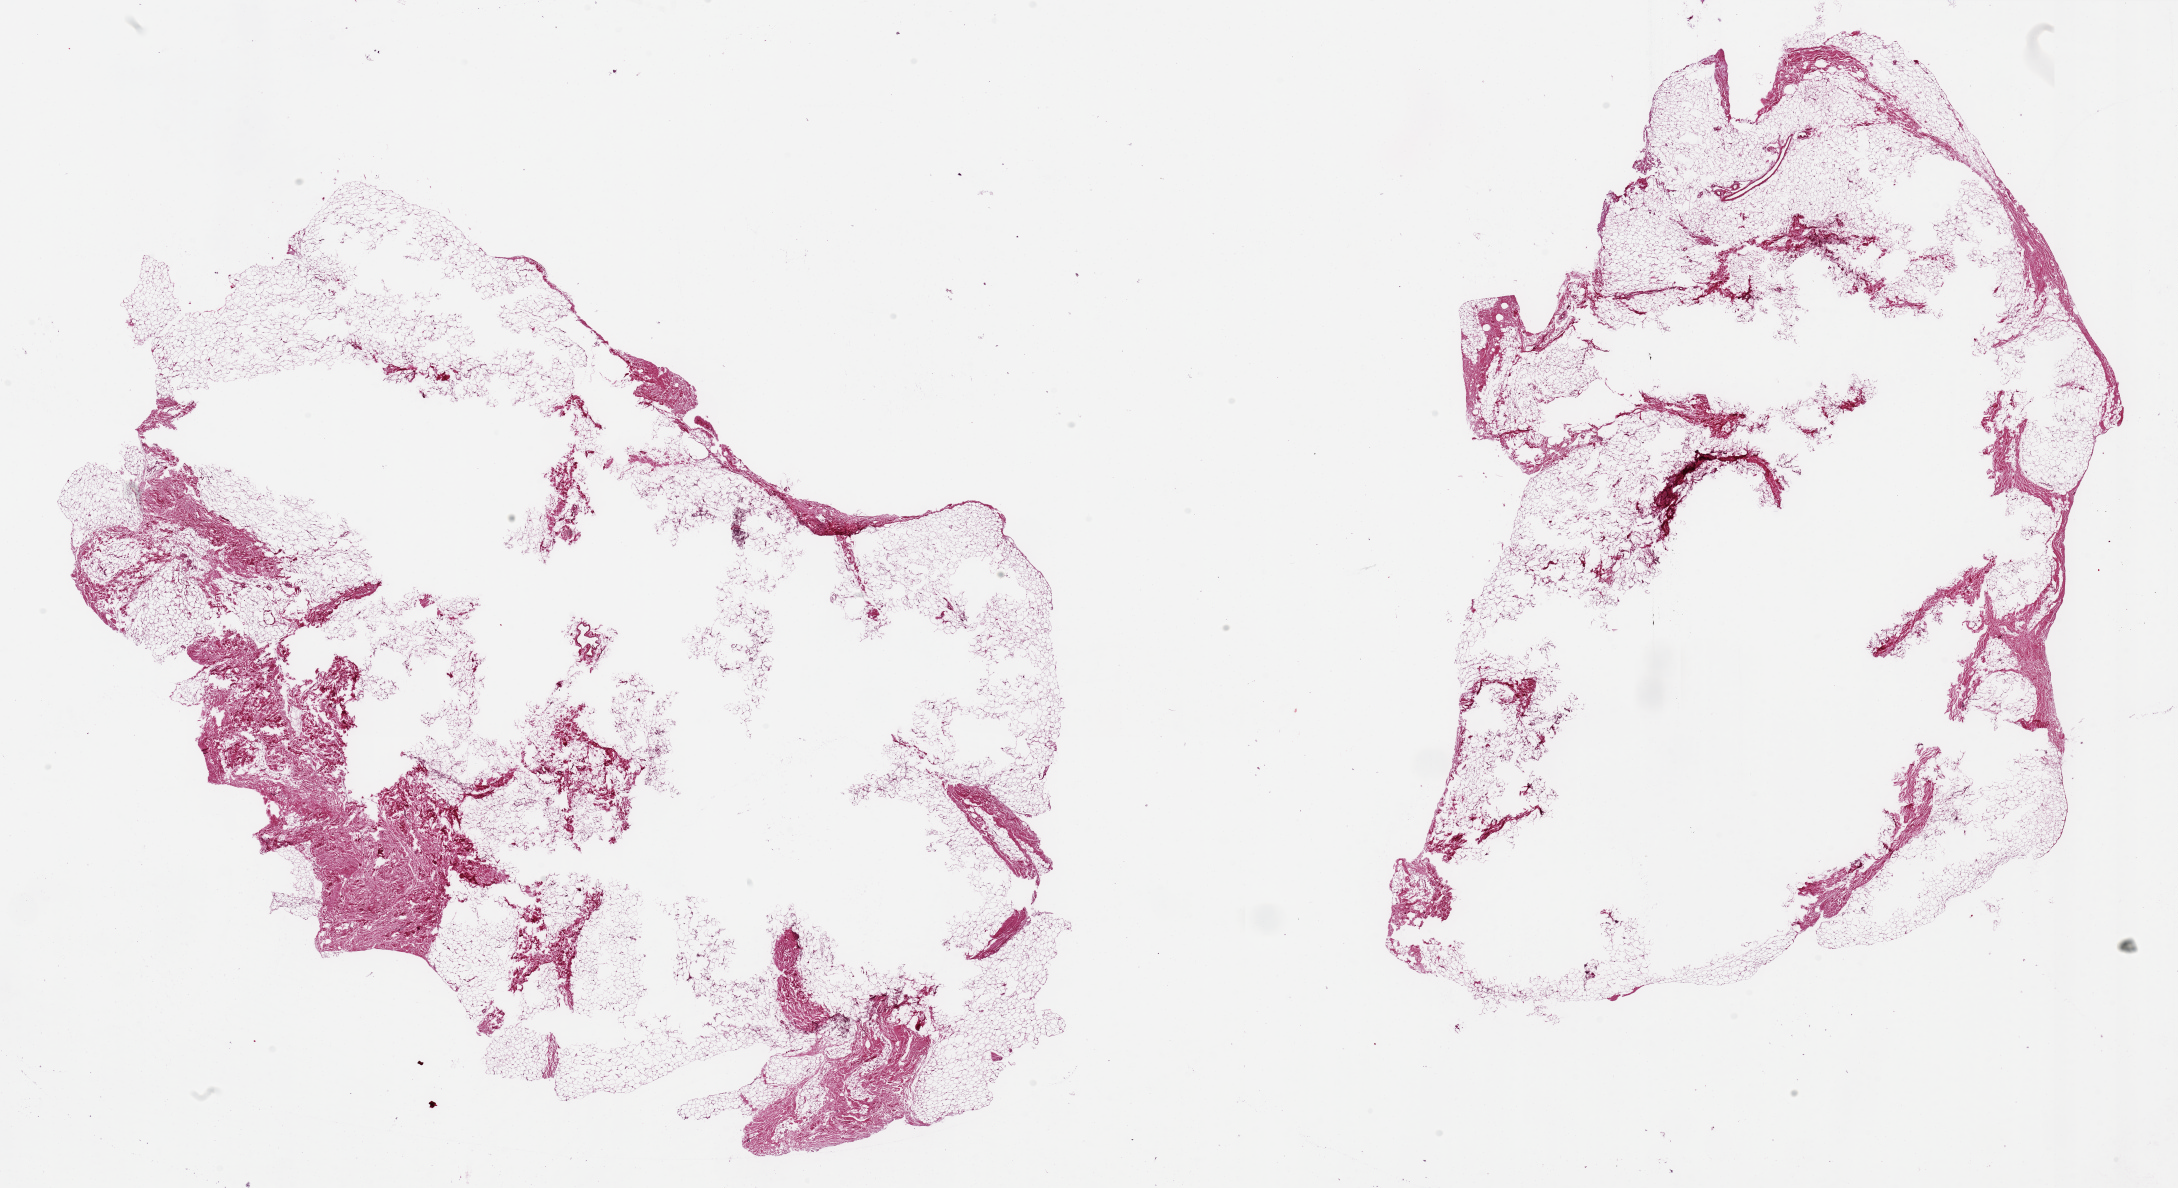
Whole-slide image, haematoxylin and eosin stain, whole scanned area (about 34.5 x 18.8 mm) shown as a low-resolution overview. PAXgene-fixed, paraffin-embedded tissue. Sampled site (target tissue): breast. Donor tissue sample. Male donor.
Reviewer comment on this tissue sample: 2 pieces 18x11 & 15x9 mm; fibroadipose tissue with no mammary ducts; excessively large aliquots with large central empty poorly fixed areas.